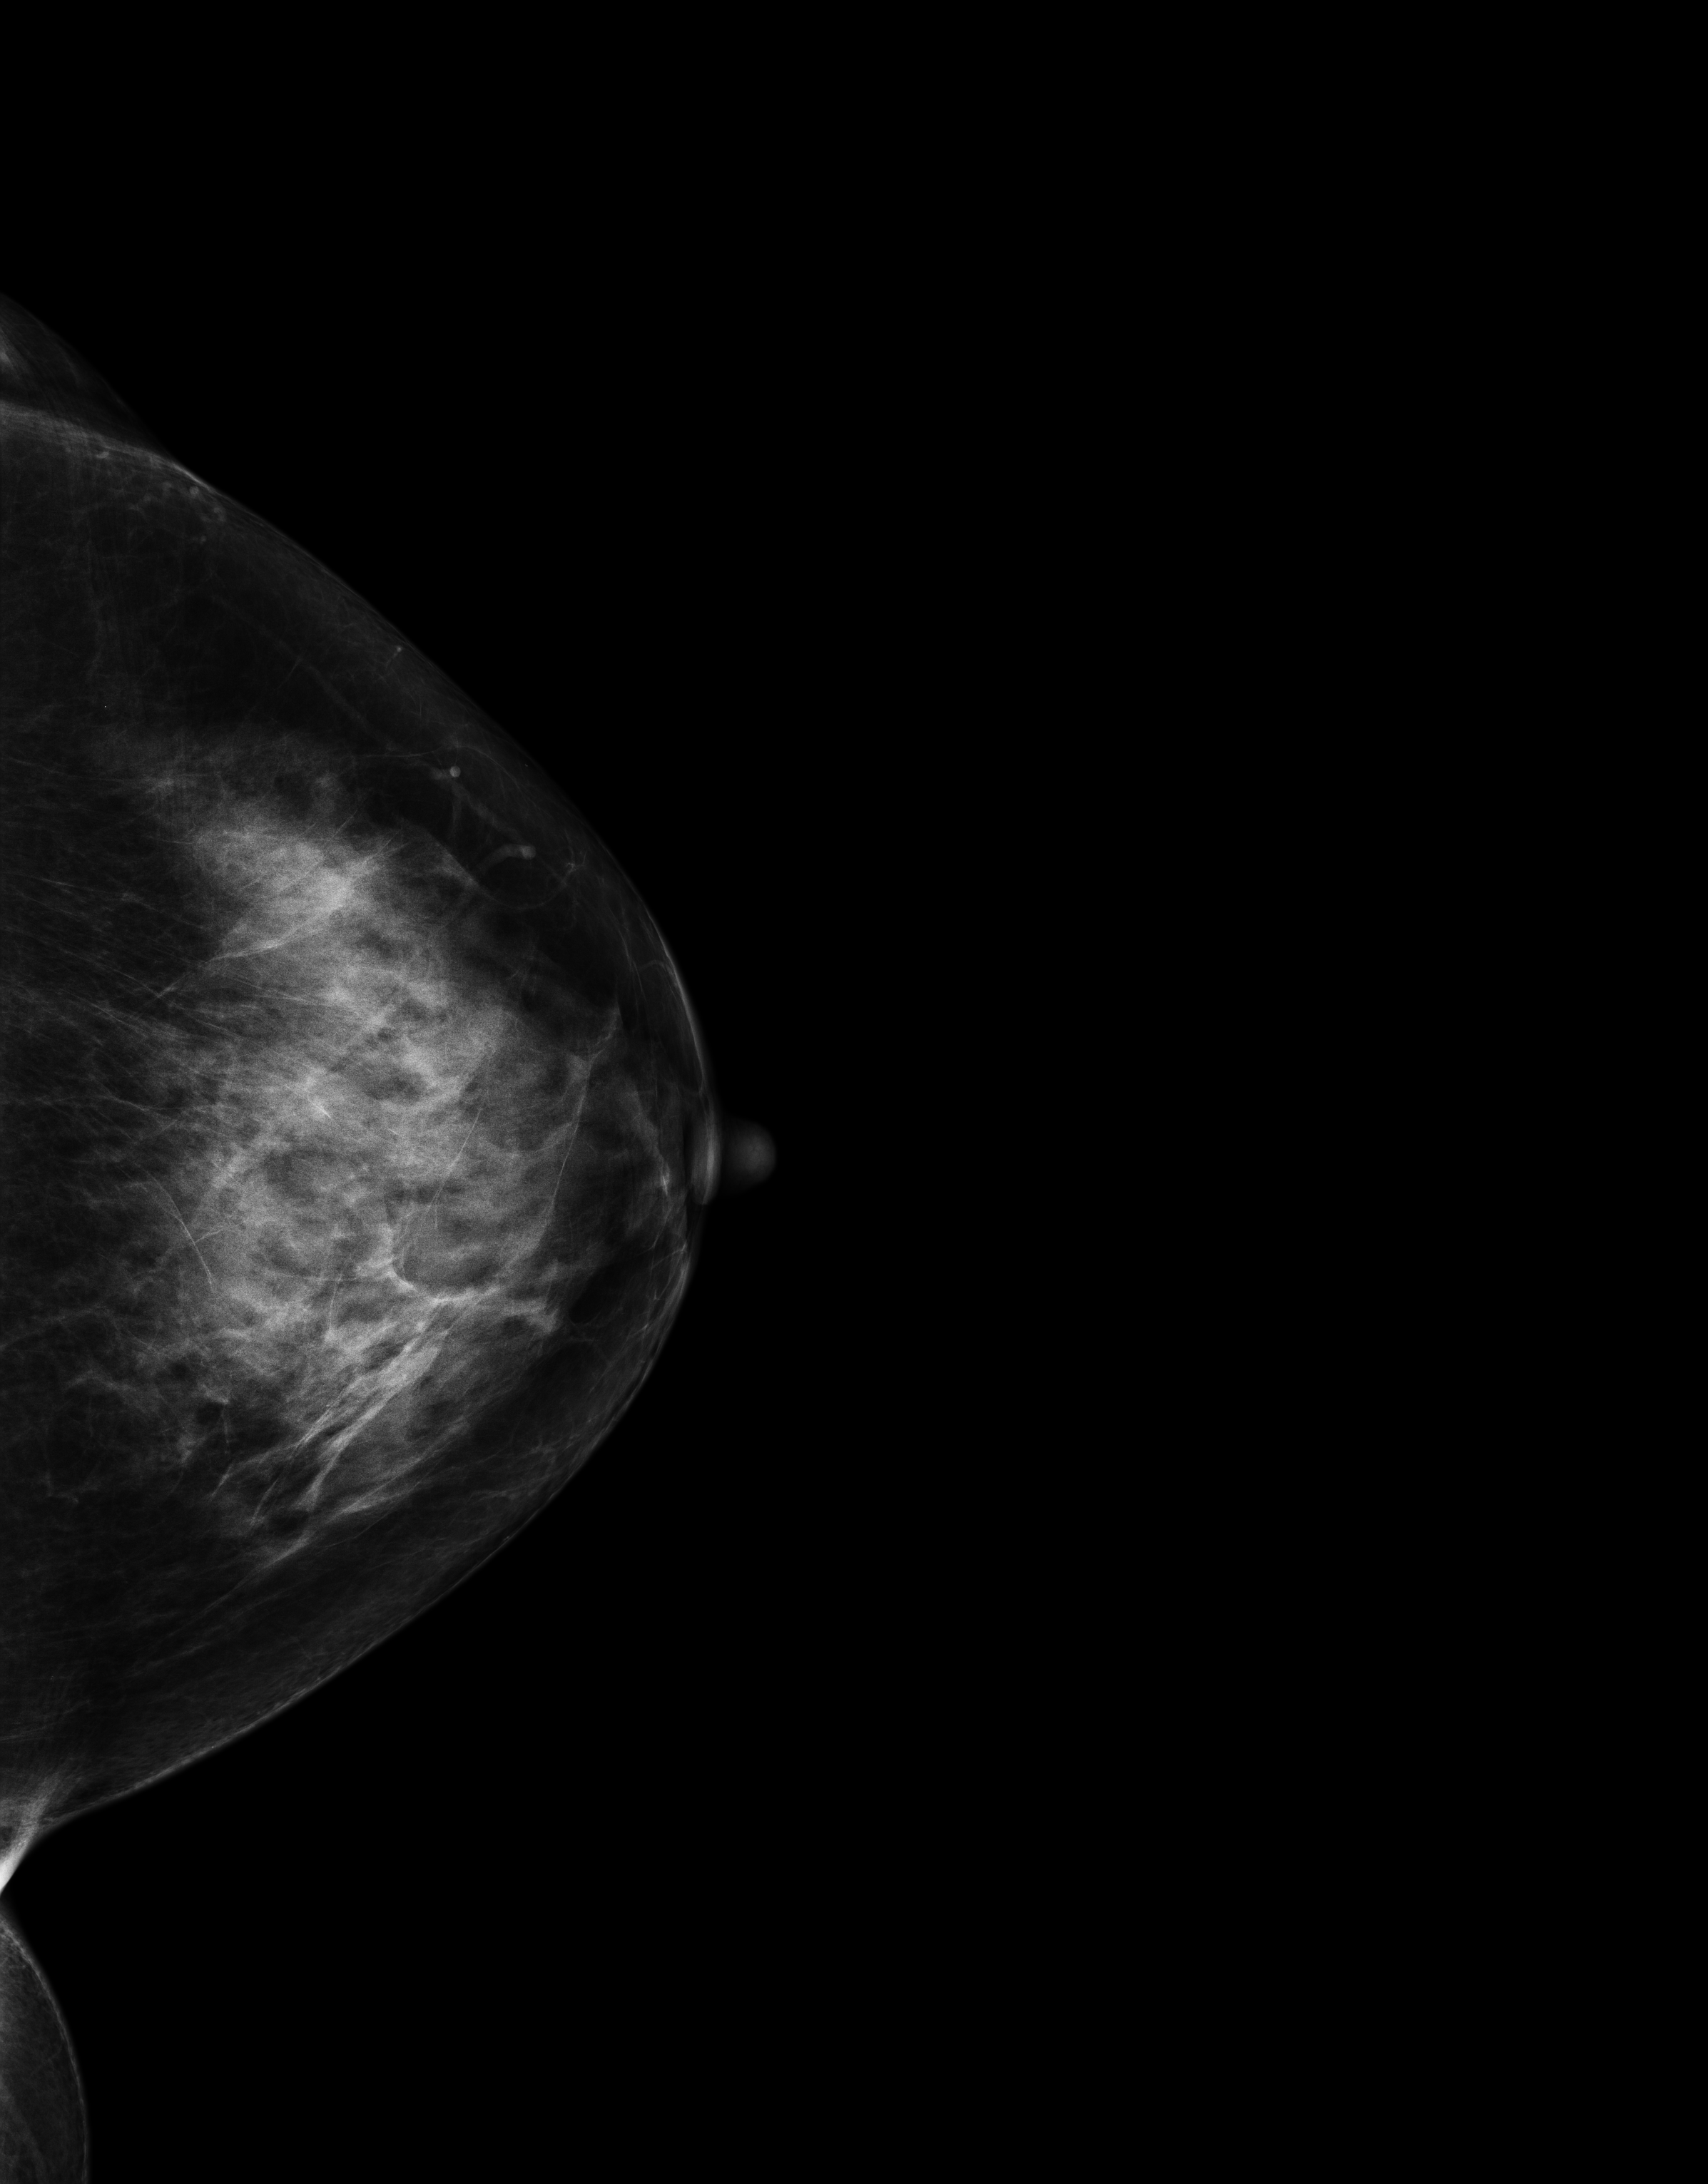
Digital mammogram (FFDM), left breast, craniocaudal (CC) view, annual screening mammography examination. Patient: female, 67 years.
Breast density at the screening exam (both breasts): heterogeneously dense (BI-RADS density category c). Final BI-RADS assessment for this screening round (tomosynthesis exam, both breasts): category 1. Recall: no recall after this screen.